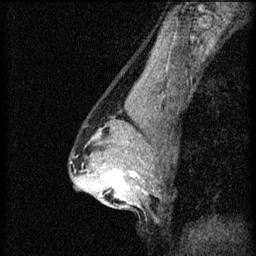
Breast MRI (dynamic contrast-enhanced), one sagittal slice; slice 40 of 60 in the series (ordered by position); 3 images stored at this slice position (order not interpretable as contrast timing); 1.5 T; TE 4.2 ms, TR 8.2 ms; 2 mm slice thickness; 256 × 256 image matrix. Female patient, age 44 years.
Annotated regions visible in this slice (semi-automatically segmented with operator editing):
- analysis volume of interest (the breast-tissue region the enhancement analysis was run in; not a lesion): bounding box [x1, y1, x2, y2] px = [94, 162, 143, 205]
- tumour enhancement mask (voxels above the 70 % enhancement threshold inside the analysis volume of interest): [100, 170, 141, 201]